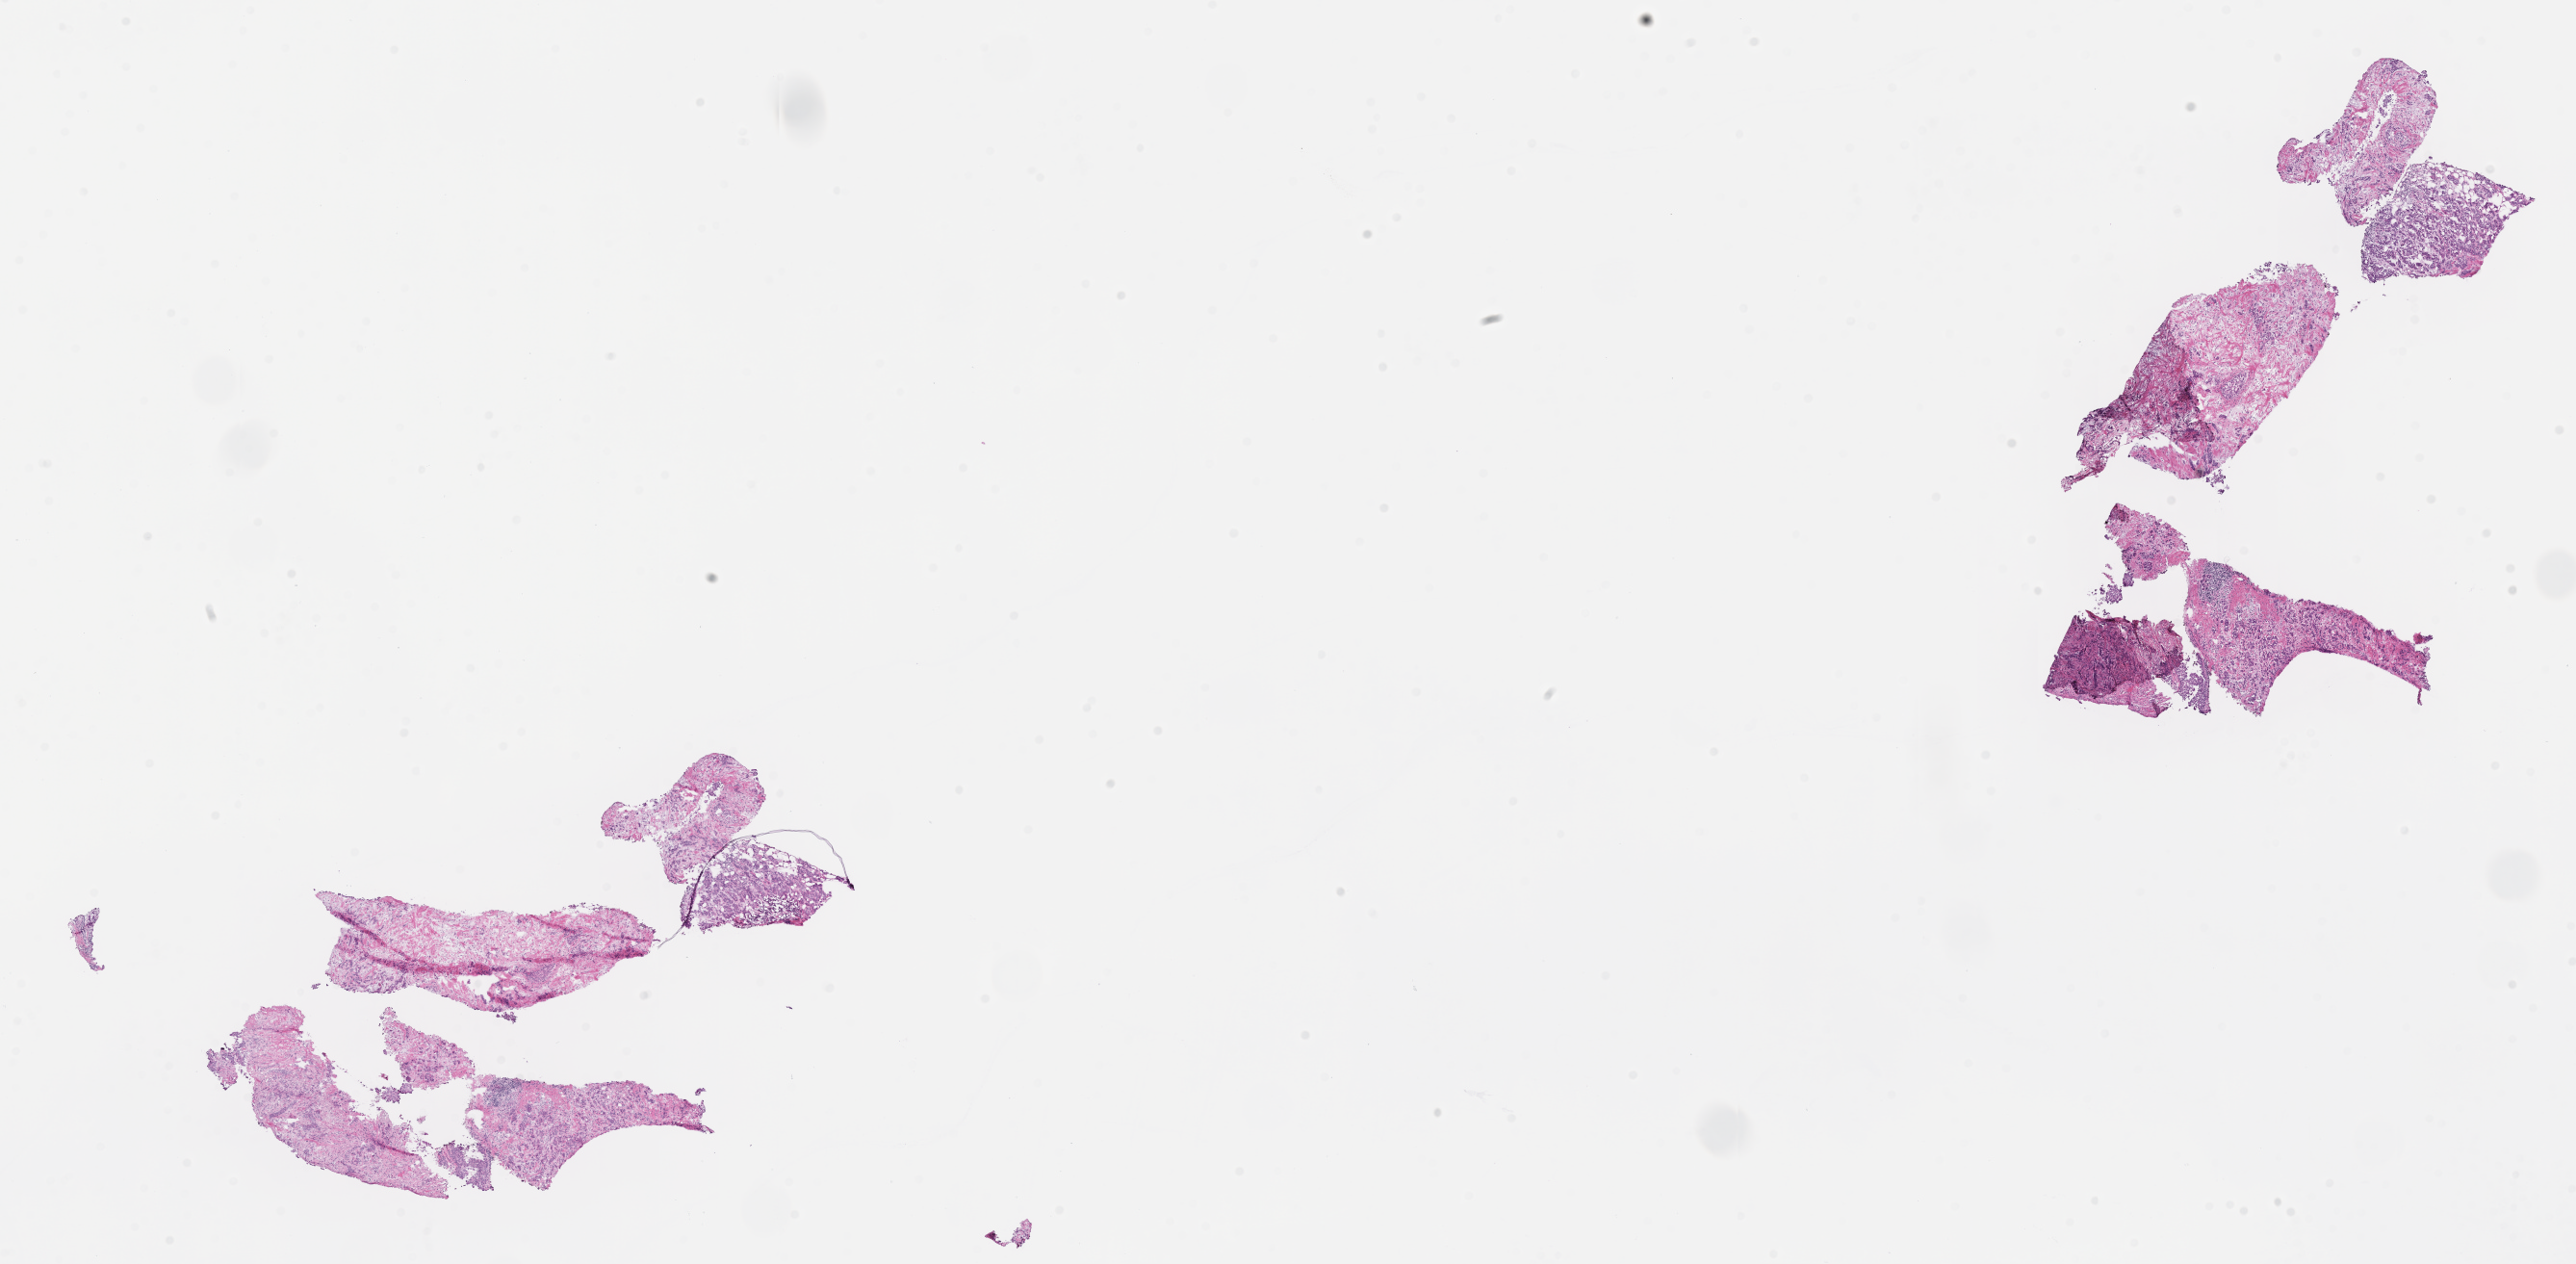
H&E whole-slide image — shown as a low-resolution overview of the whole scanned area (about 21.6 x 10.6 mm). Frozen section. Specimen: primary tumor. Site: breast (left). Female, age 55 years at initial diagnosis. Slide review estimates, as recorded: tumor cells 45%, tumor nuclei 45%, stromal cells 40%, necrosis 5%, normal cells 10%. Inflammatory infiltration, as recorded: lymphocyte infiltration 5%, monocyte infiltration 2%, neutrophil infiltration 2%.
Histologic diagnosis: Infiltrating duct carcinoma, NOS.